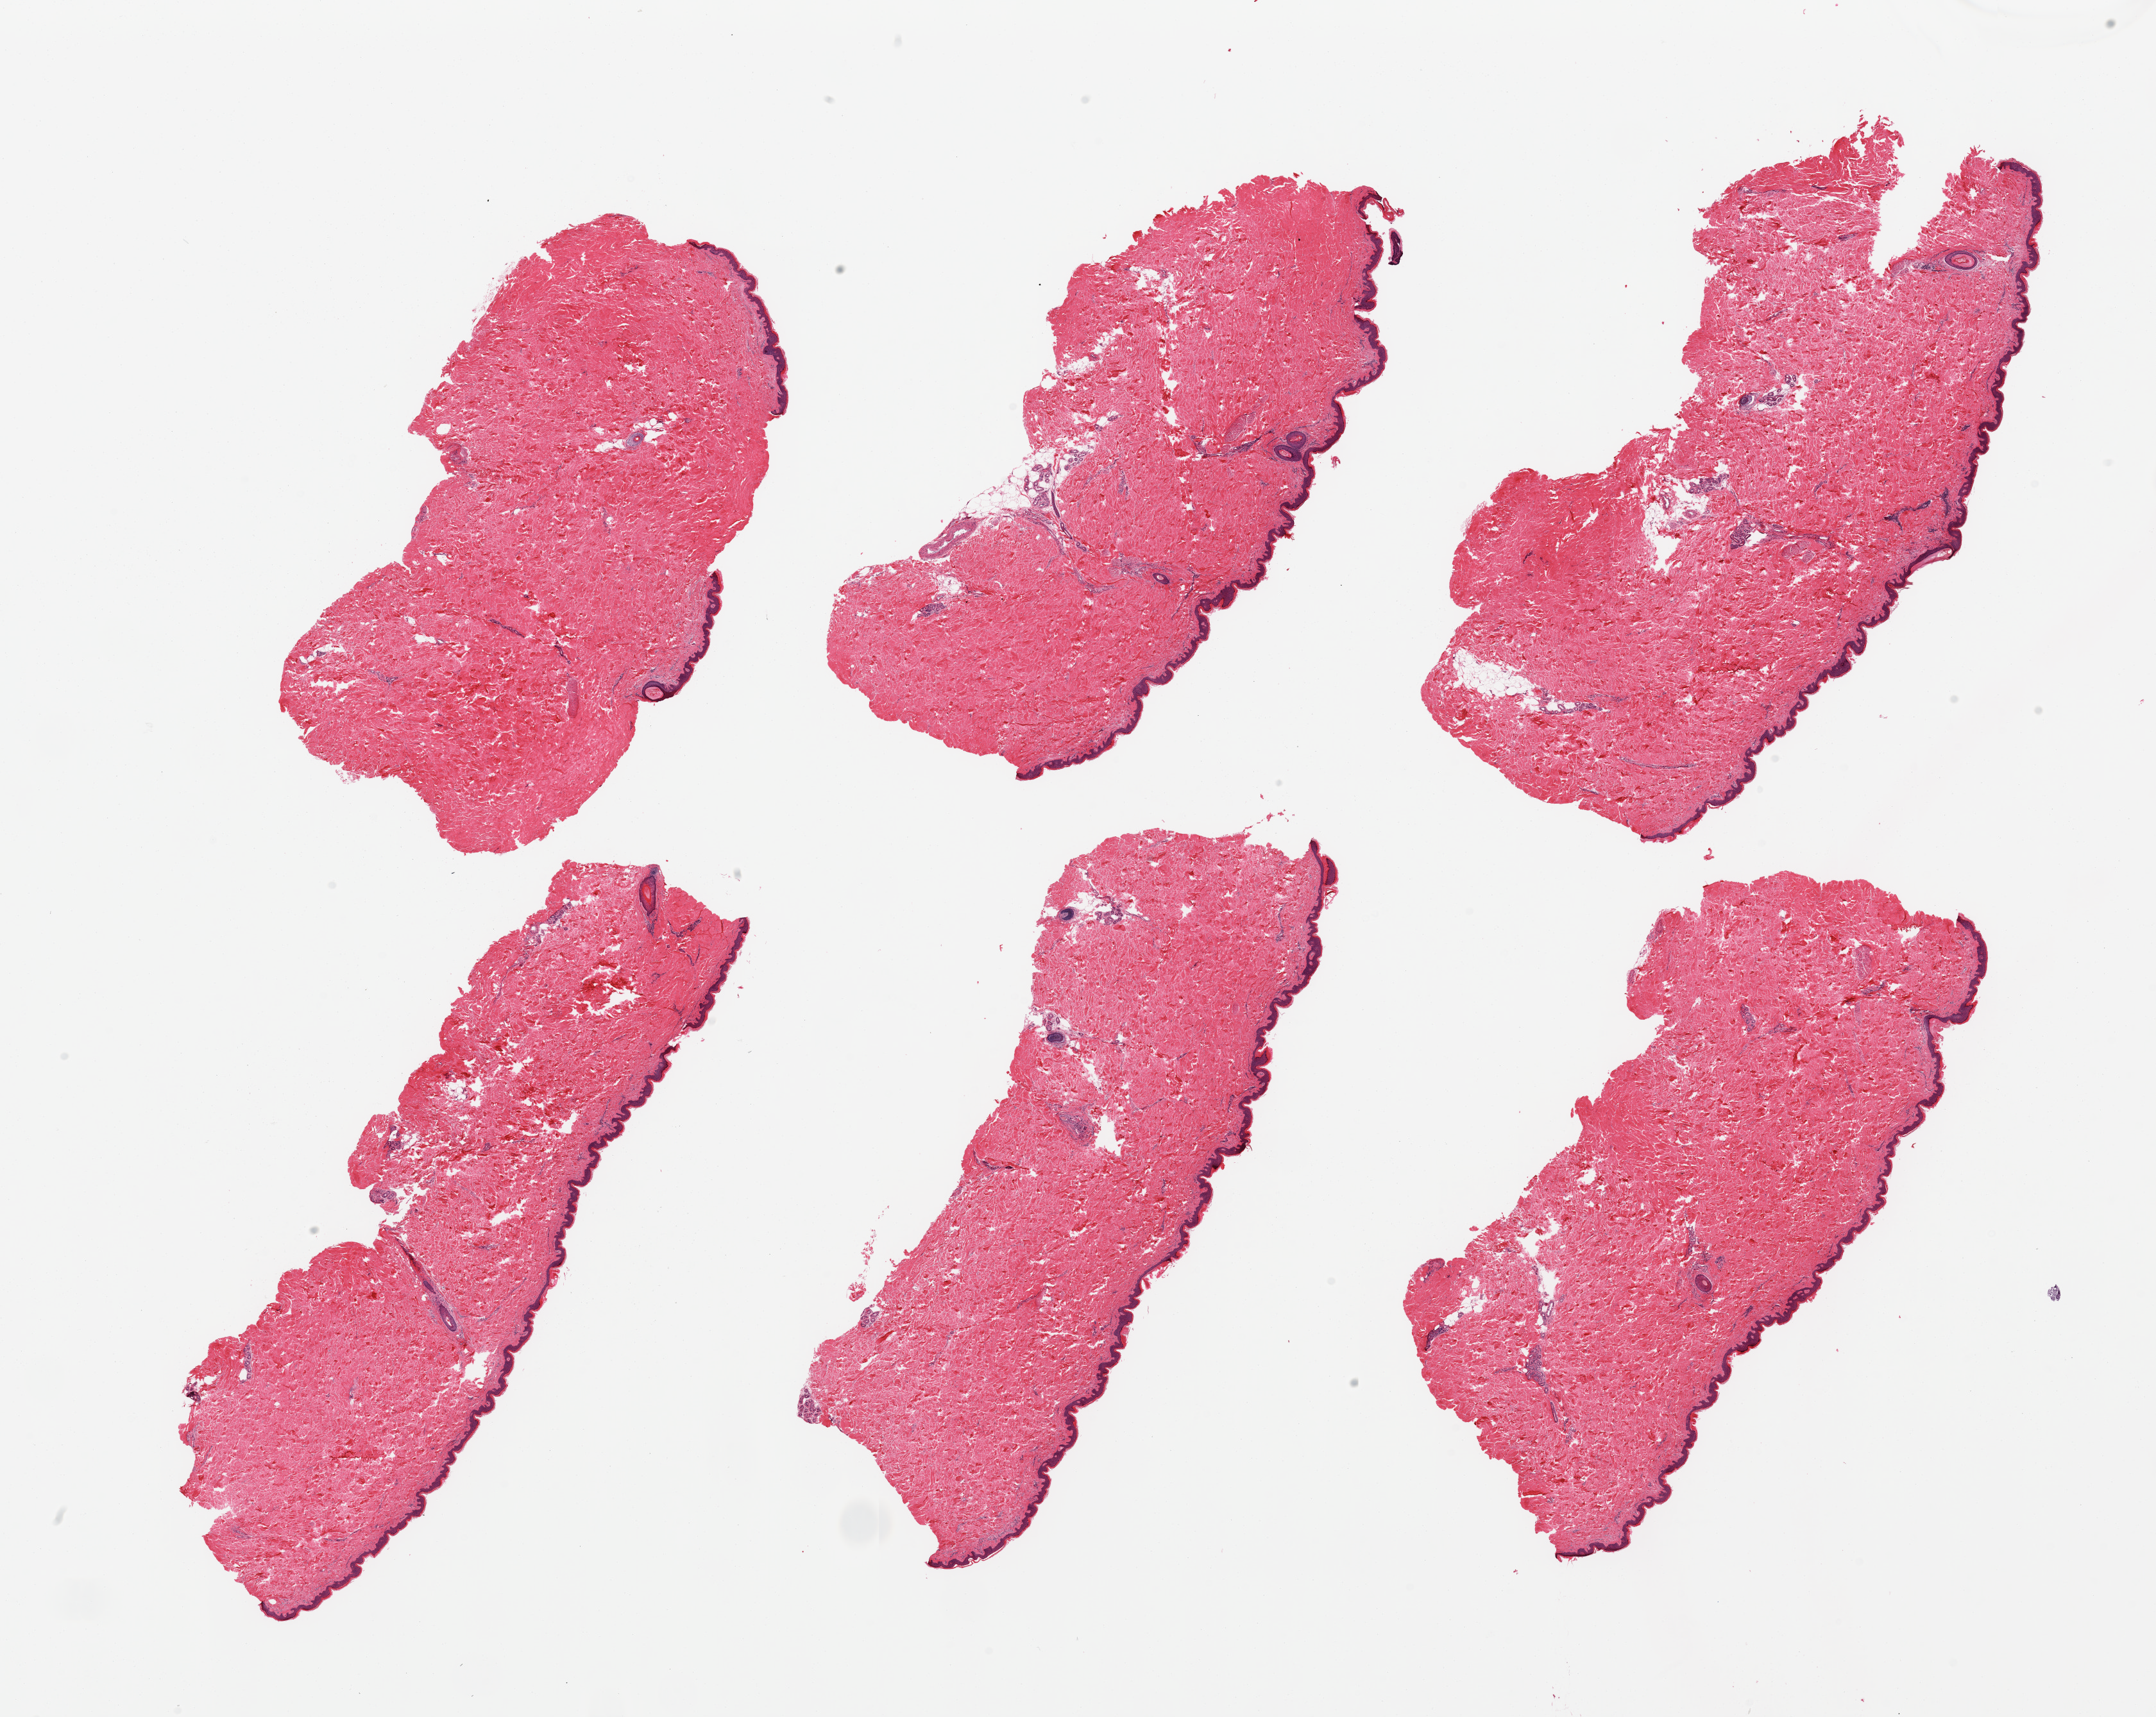
Whole-slide image, haematoxylin and eosin stain, whole scanned area (about 26.6 x 21.2 mm) shown as a low-resolution overview, PAXgene-fixed, paraffin-embedded tissue, section of skin of suprapubic region (target tissue), tissue donor sample.
Pathologist's review note for this sample: 6 pieces, no significant dermal fat; squamous epithelium is ~50-60 microns.